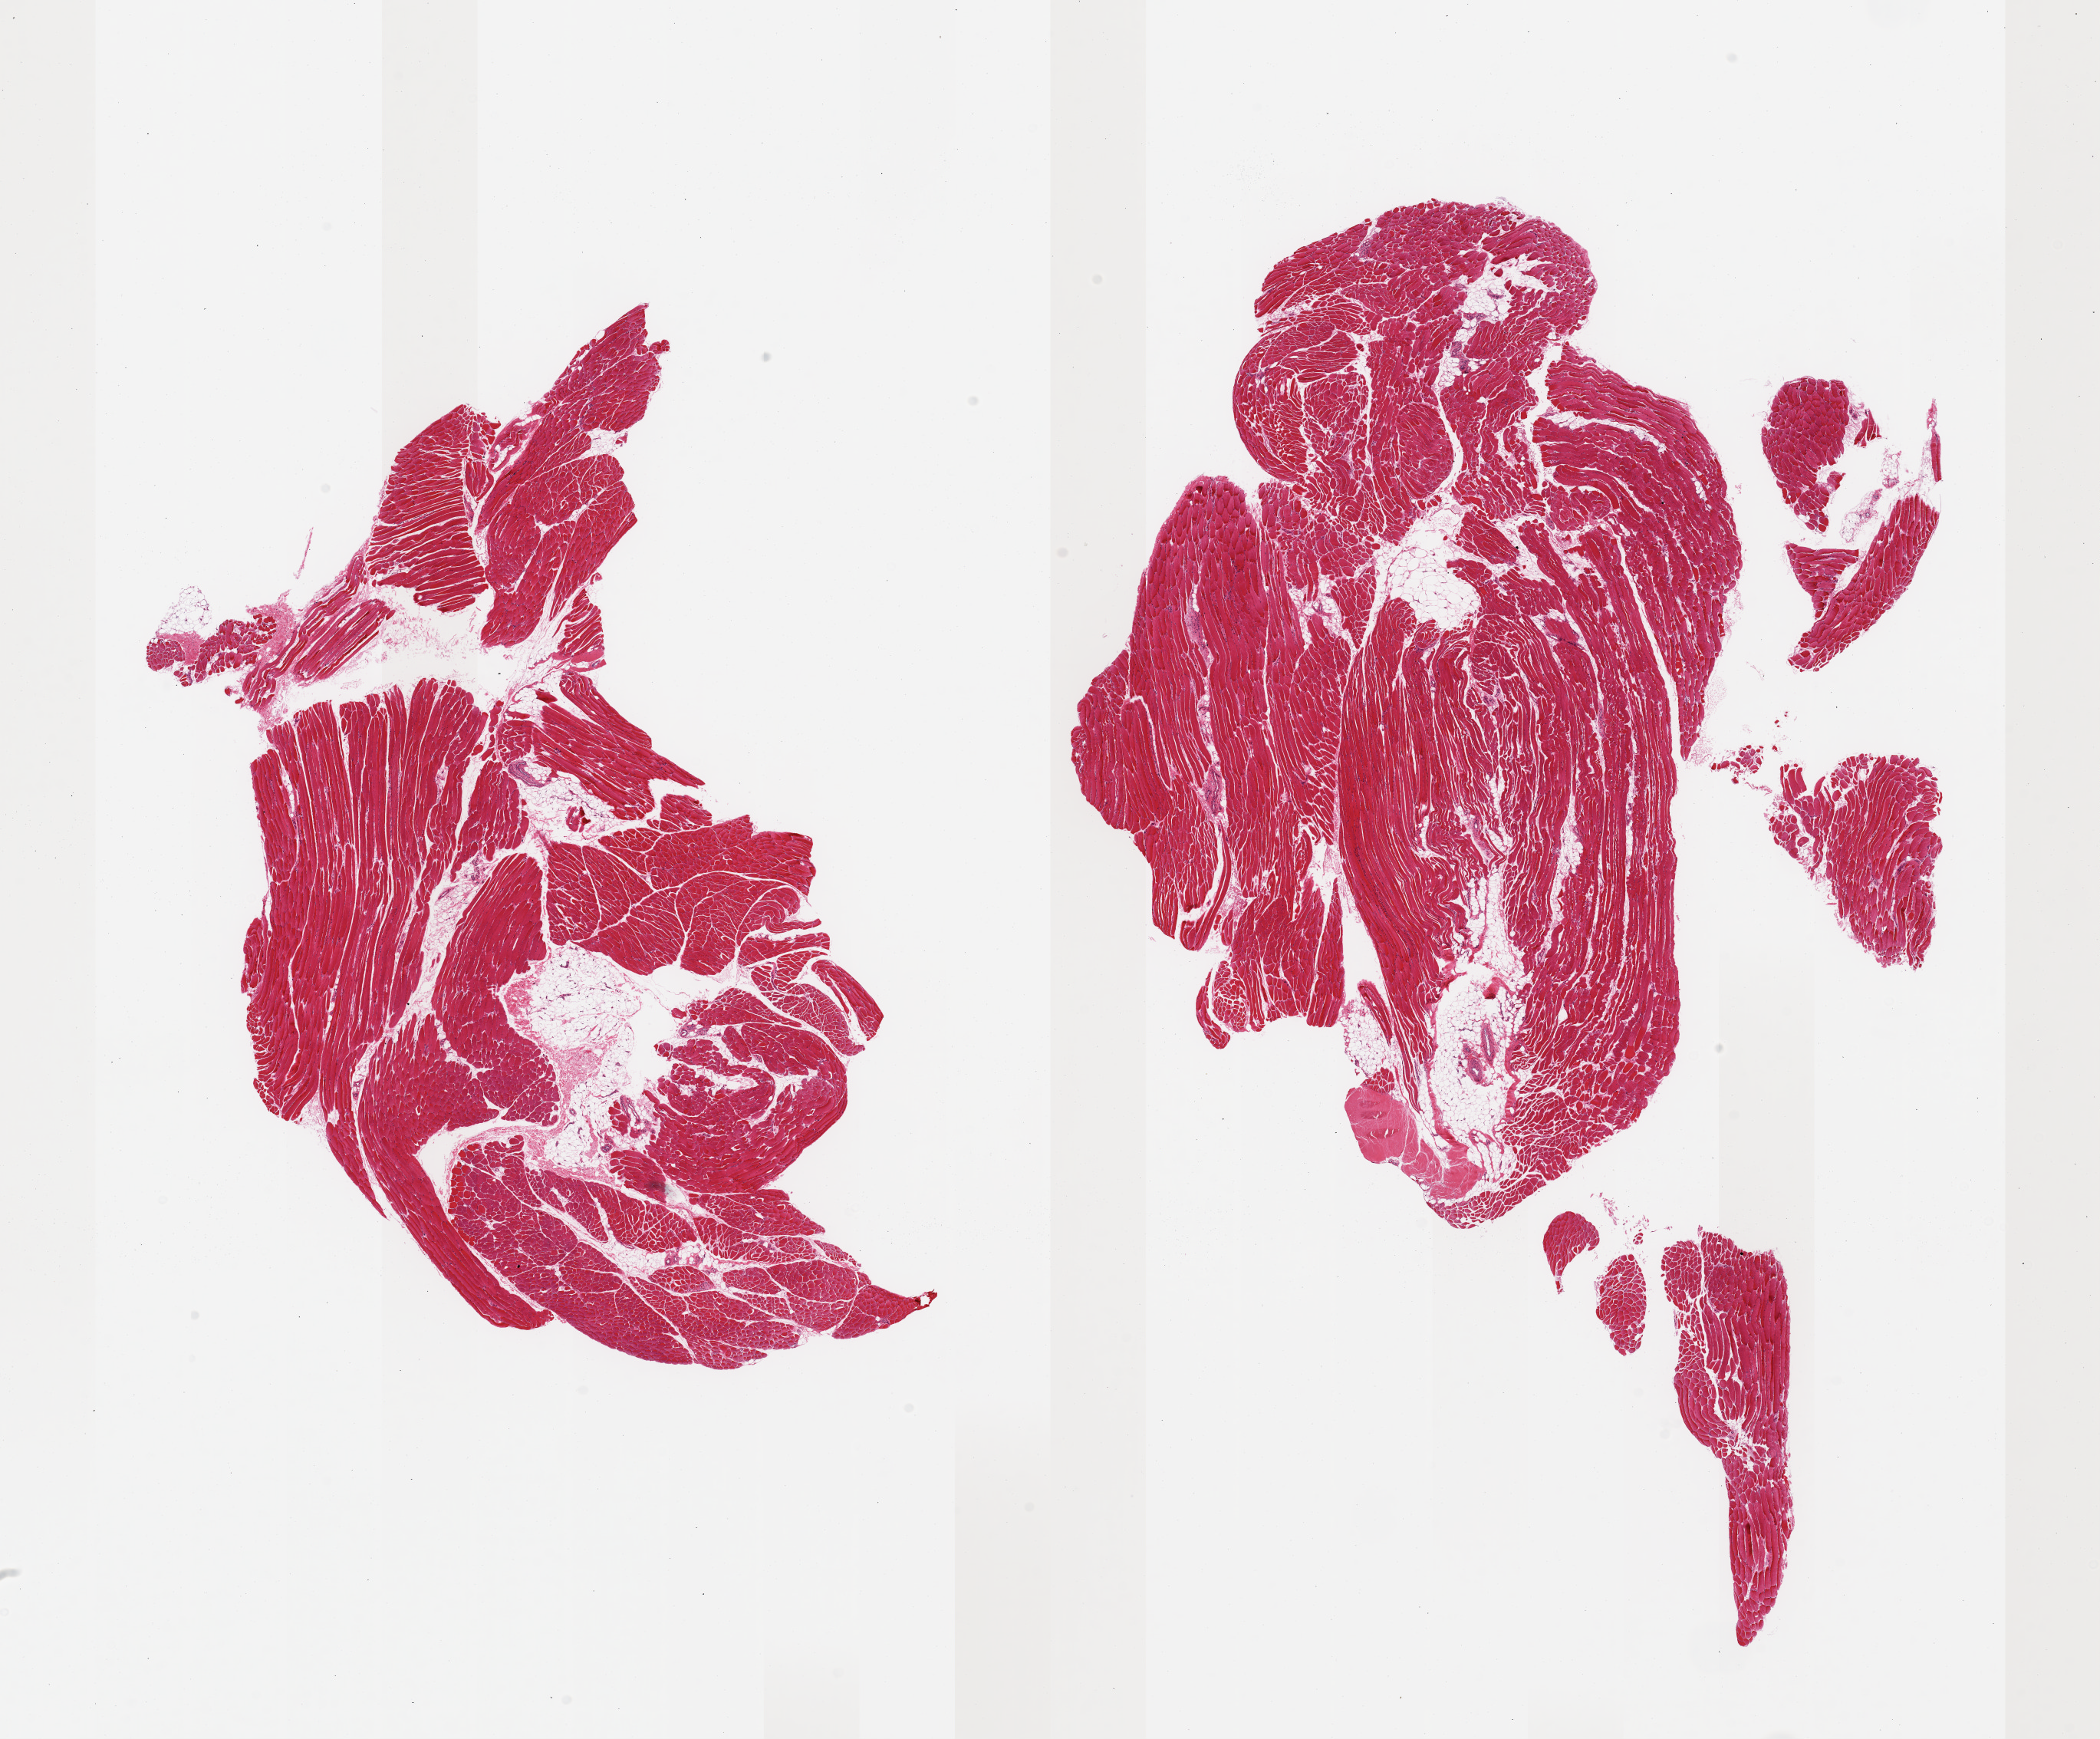
Digitized H&E-stained section, shown as a low-resolution overview of the whole scanned area (about 21.7 x 17.9 mm); PAXgene-fixed paraffin-embedded (PFPE) section; target tissue: skeletal muscle; tissue donor sample. Donor sex: female.
Pathologist's review note for this sample: 2 pieces plus fragments; 10% internal fat content.